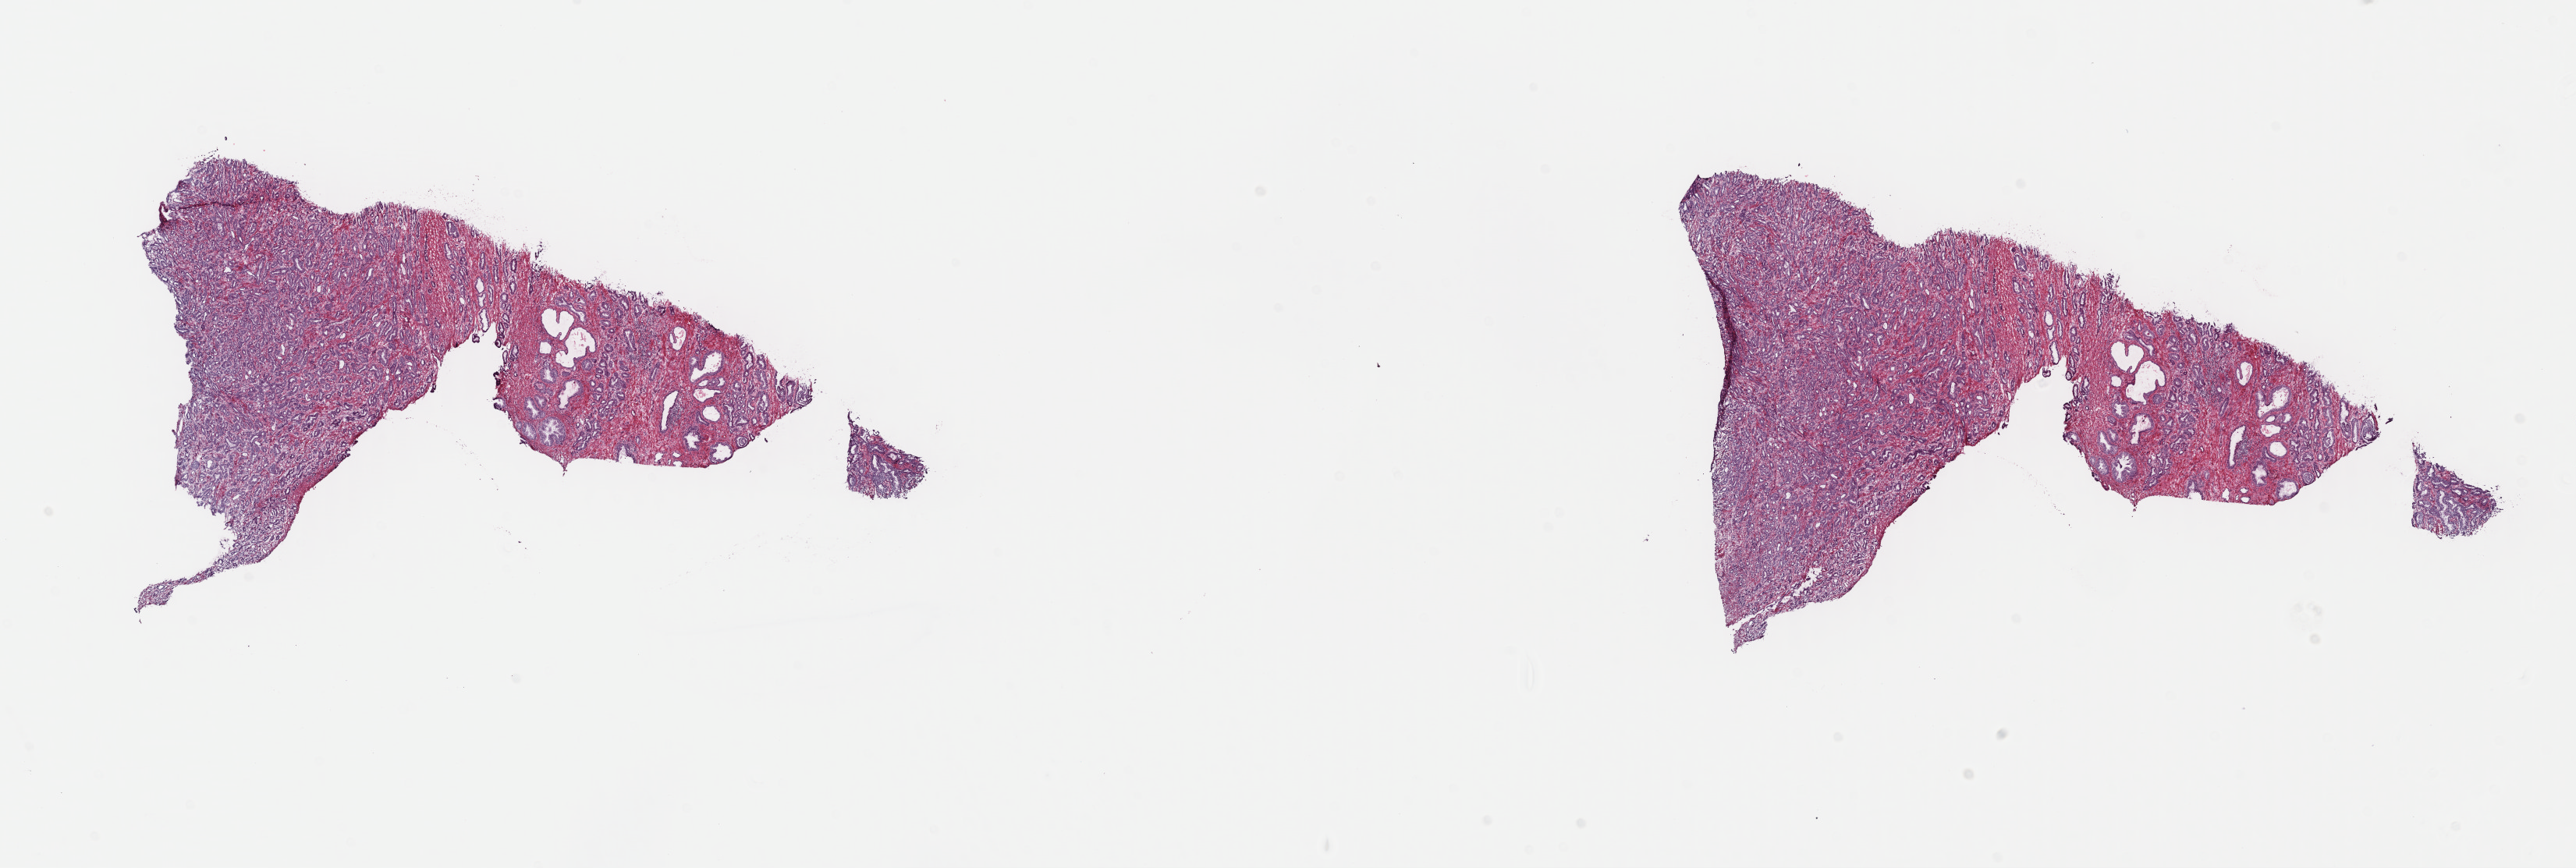
Digitized H&E-stained tissue section (whole slide), a low-resolution overview of the entire scanned area, about 26.0 x 8.7 mm (slide scanned at 40x); frozen section from the top of the tissue portion; prostate, primary tumour sample. Patient: male, age at initial diagnosis 56 years. Gleason score: 7 (3+4). Pathologist review of this section (percent, as recorded): tumour cells 80%, tumour nuclei 60%, normal cells 7%, stromal cells 13%, necrosis 0%. Infiltration values recorded for this section: lymphocyte infiltration 0%, monocyte infiltration 0%, neutrophil infiltration 0%.
* diagnosis: Adenocarcinoma, NOS (prostate gland)